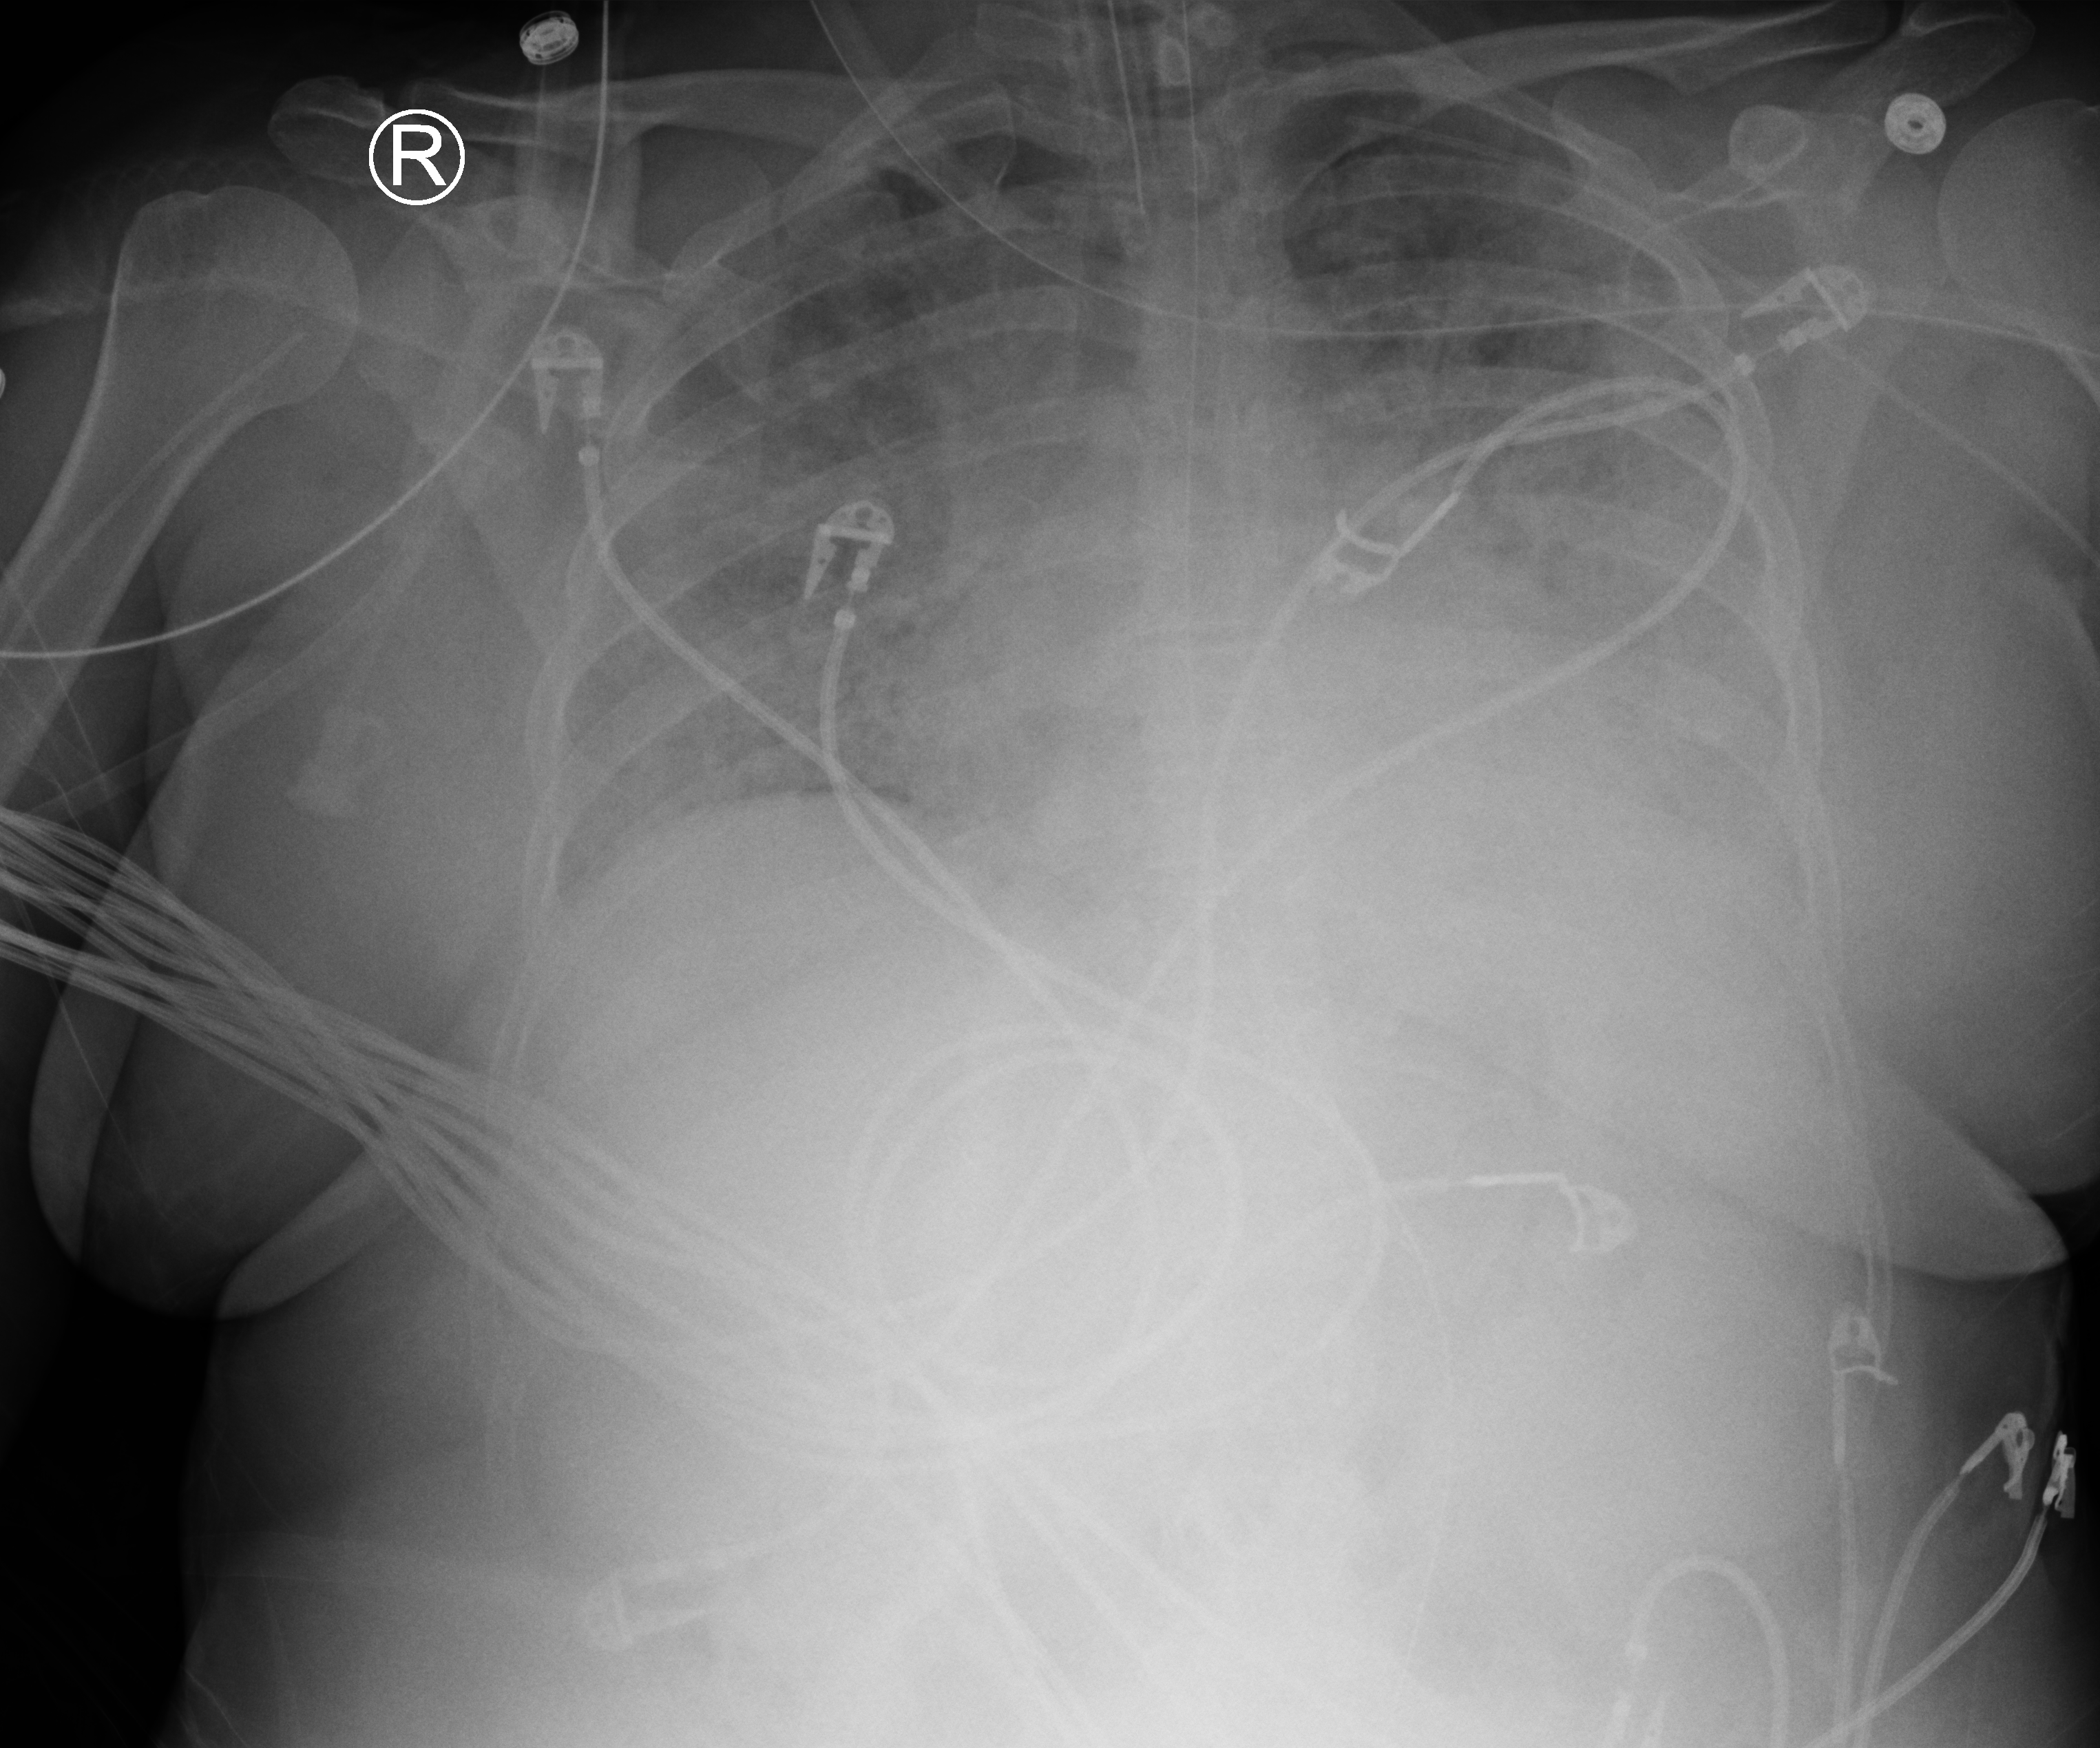
Chest X-ray (portable). Female patient hospitalised with COVID-19, age 18–59 years.
Admission-level facts for this patient (not findings on this image; timing relative to this image not recorded):
- hypertension (admission record): yes
- smoking status (admission record): never